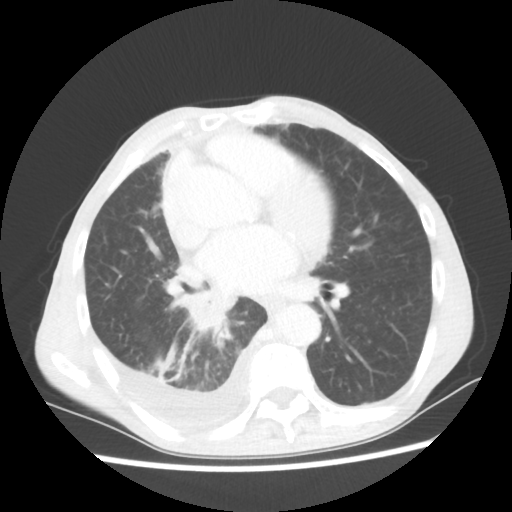
Chest CT, one axial slice; reconstruction kernel STANDARD; 80 kVp; lung window (W 1500 / L -600 HU); 5 mm slice thickness; 512 × 512 image matrix, field of view 335 × 335 mm. Male patient, age 76 years. Case-level facts recorded for this patient, not image findings: clinical TNM (as recorded): T3 N3 M1a.
Structures marked on this image (bounding box drawn by a radiologist):
- lung tumour (recorded histology: squamous cell carcinoma): bounding box [x1, y1, x2, y2] px = [173, 288, 235, 350]